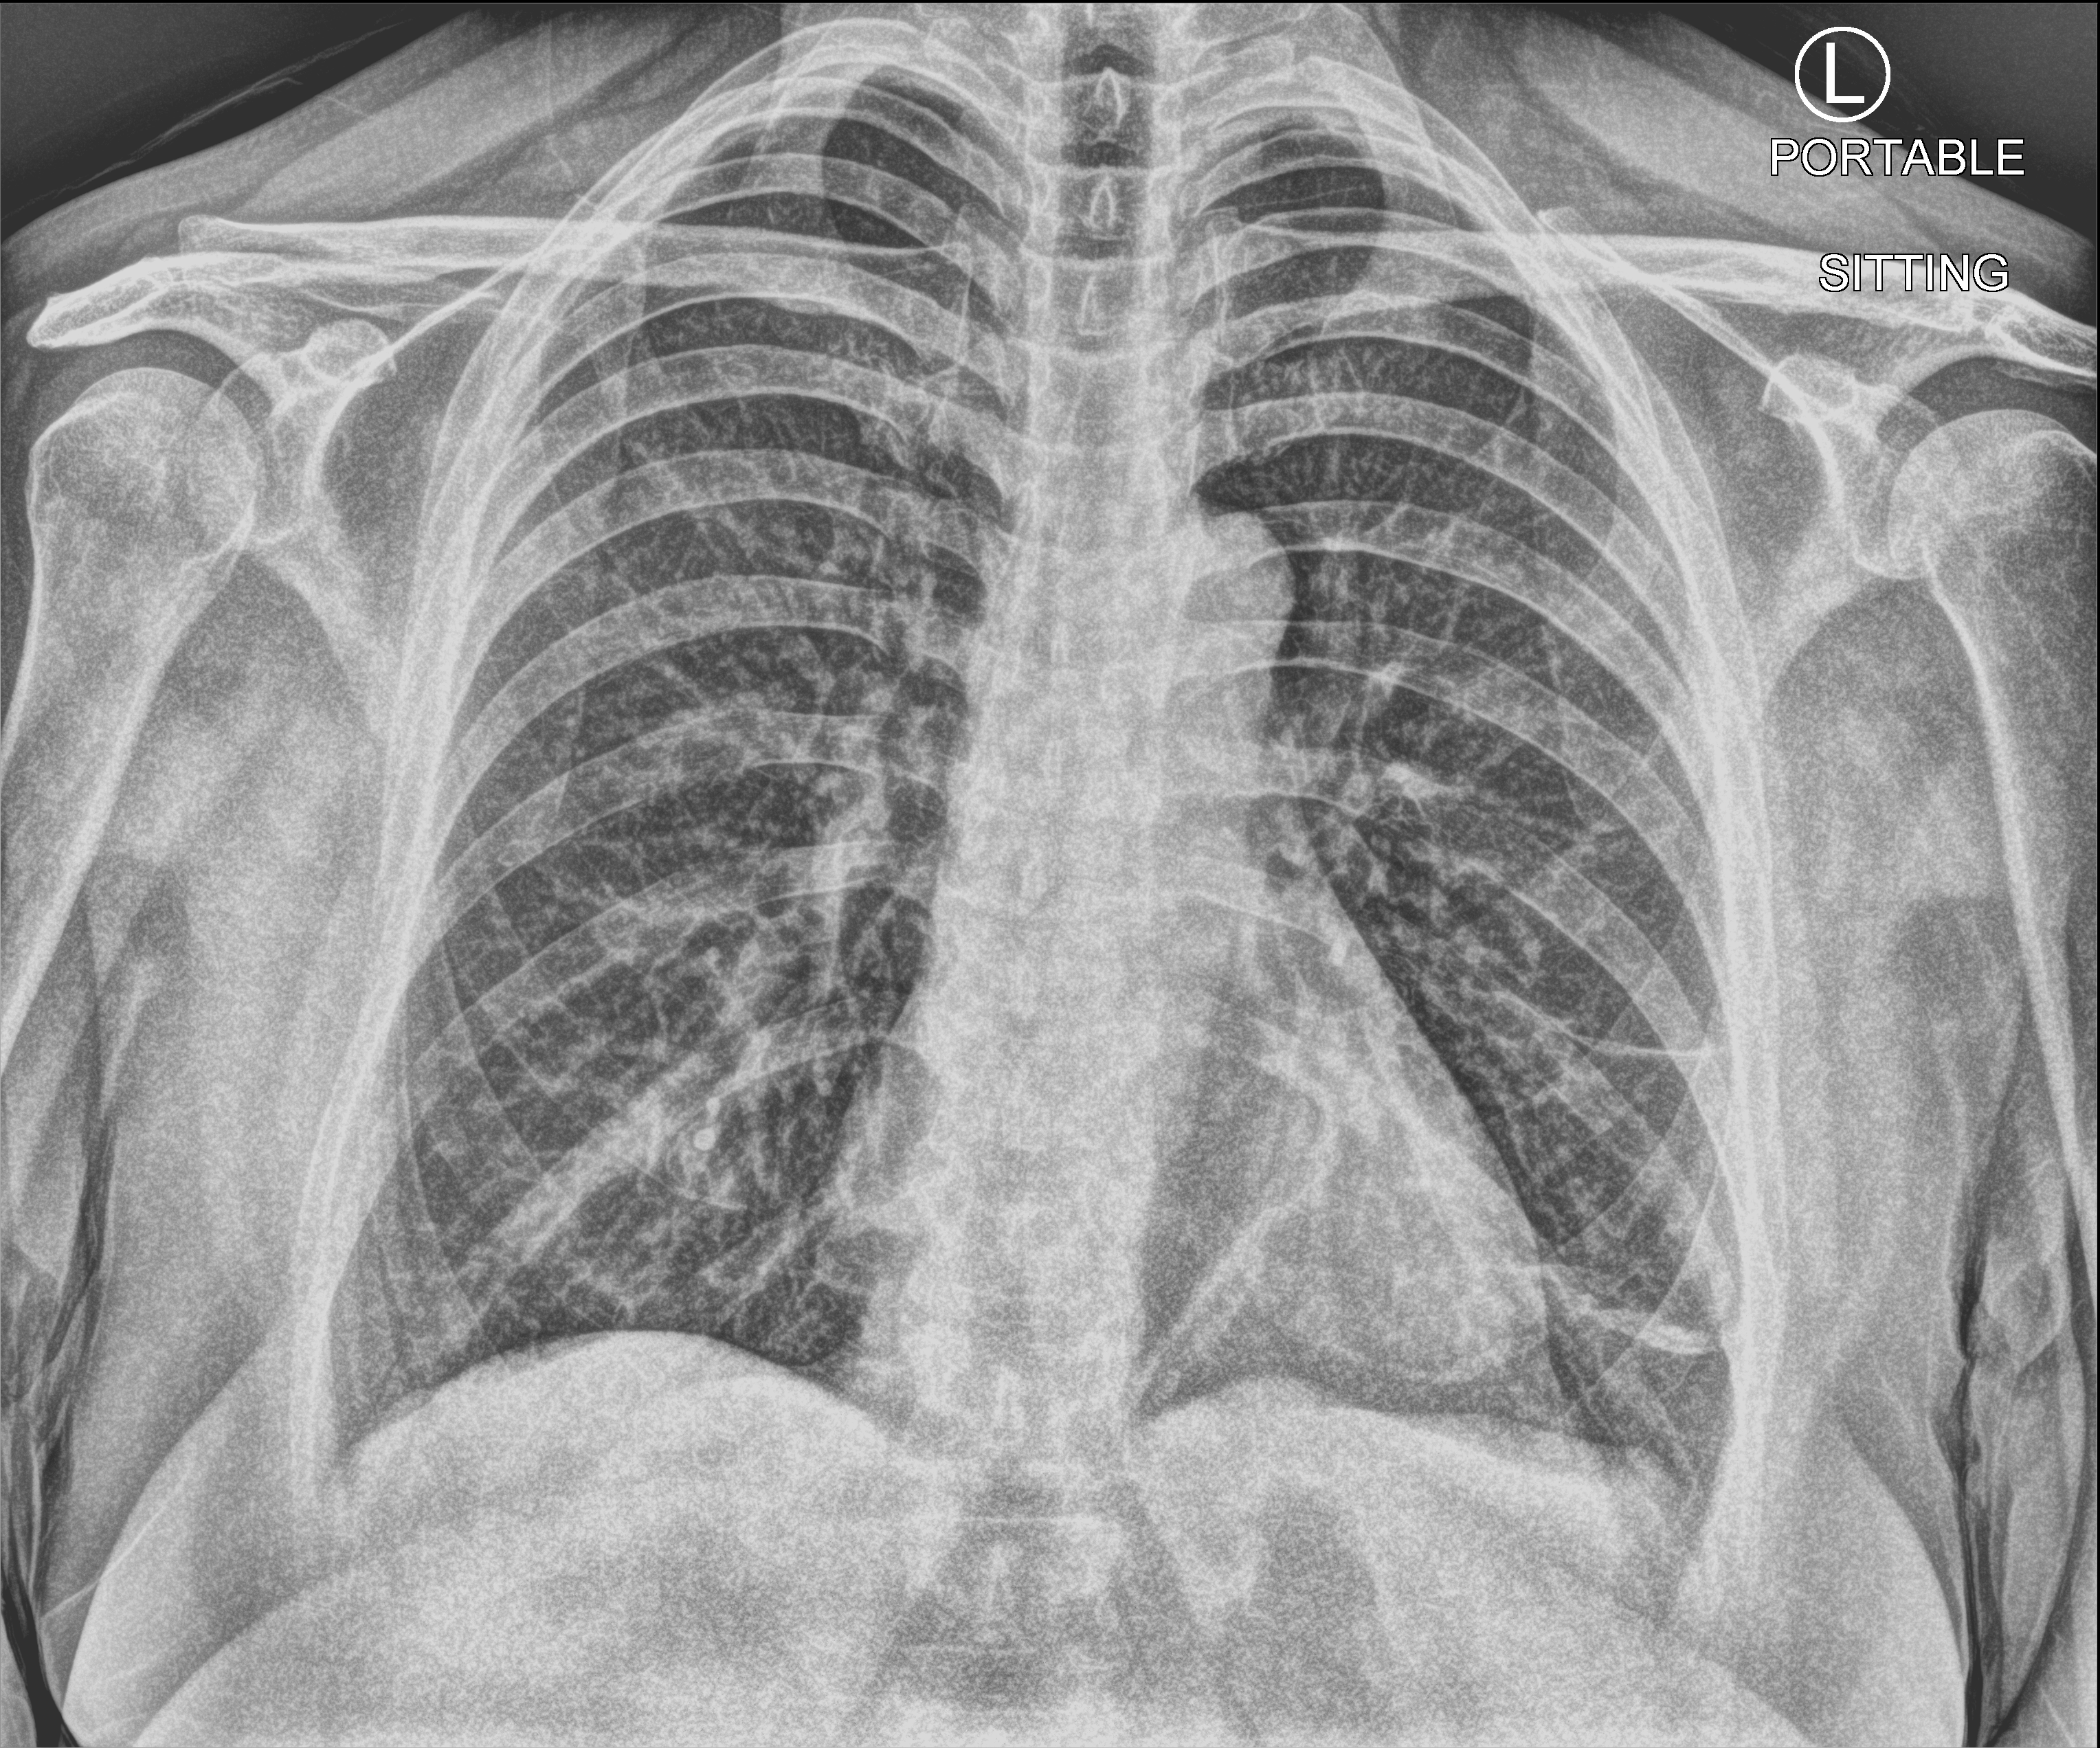
Portable chest radiograph, anteroposterior (AP) projection. Patient hospitalised with COVID-19; female, aged 18–59 years.
Hospital-stay facts (about this admission, not read from this image; timing relative to this image not recorded): admitted to intensive care during this hospital stay: no; mechanically ventilated during this hospital stay: no.